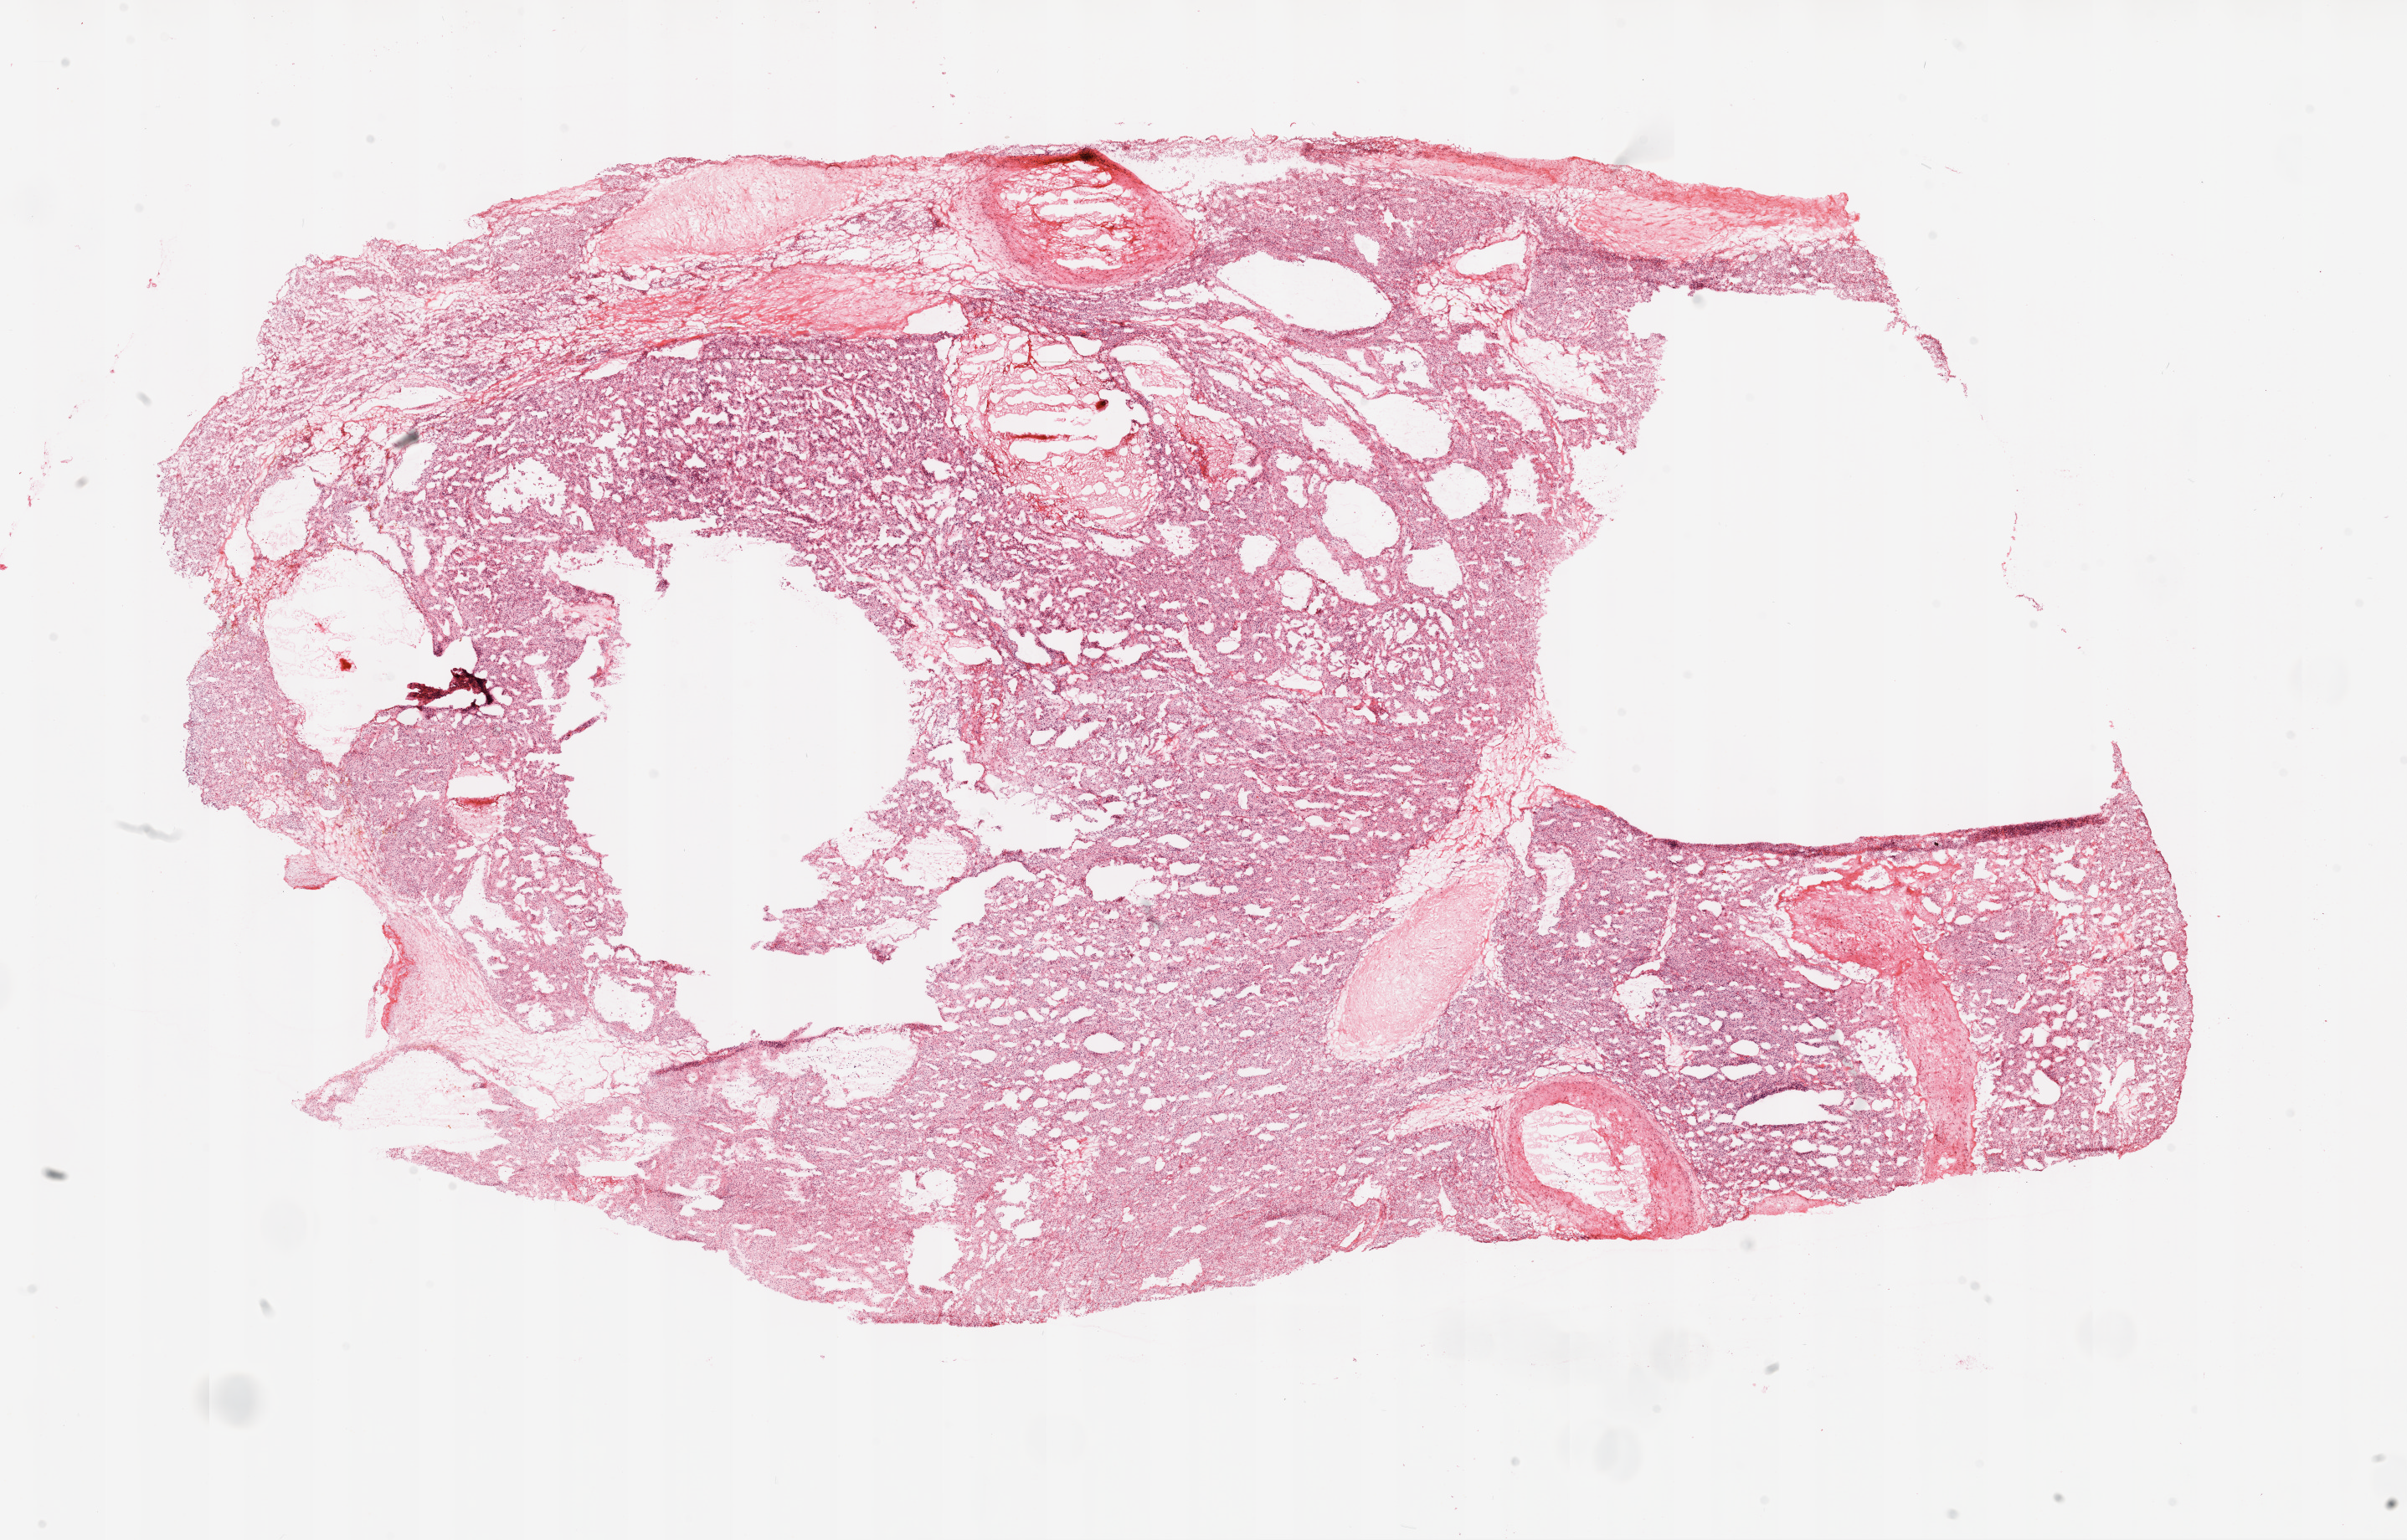
Whole-slide histology image, Hematoxylin and eosin (H&E) stained, whole scanned area (about 23.1 x 14.8 mm, slide scanned at 20x) shown as a low-resolution overview, frozen section from the top of the tissue portion, kidney, primary tumour sample. Male patient; age at initial diagnosis 63 years. Histologic grade: G2 (moderately differentiated). Pathologist review of this section (percent, as recorded): tumour cells 90%, tumour nuclei 90%, normal cells 0%, stromal cells 10%, necrosis 0%. Inflammatory infiltration, as recorded: lymphocyte infiltration 2%, monocyte infiltration 0%, neutrophil infiltration 0%.
Laterality: right. Histologic diagnosis: Clear cell adenocarcinoma, NOS. AJCC pathologic stage: IV. Lymph nodes positive (case pathology): 0 of 3 examined.